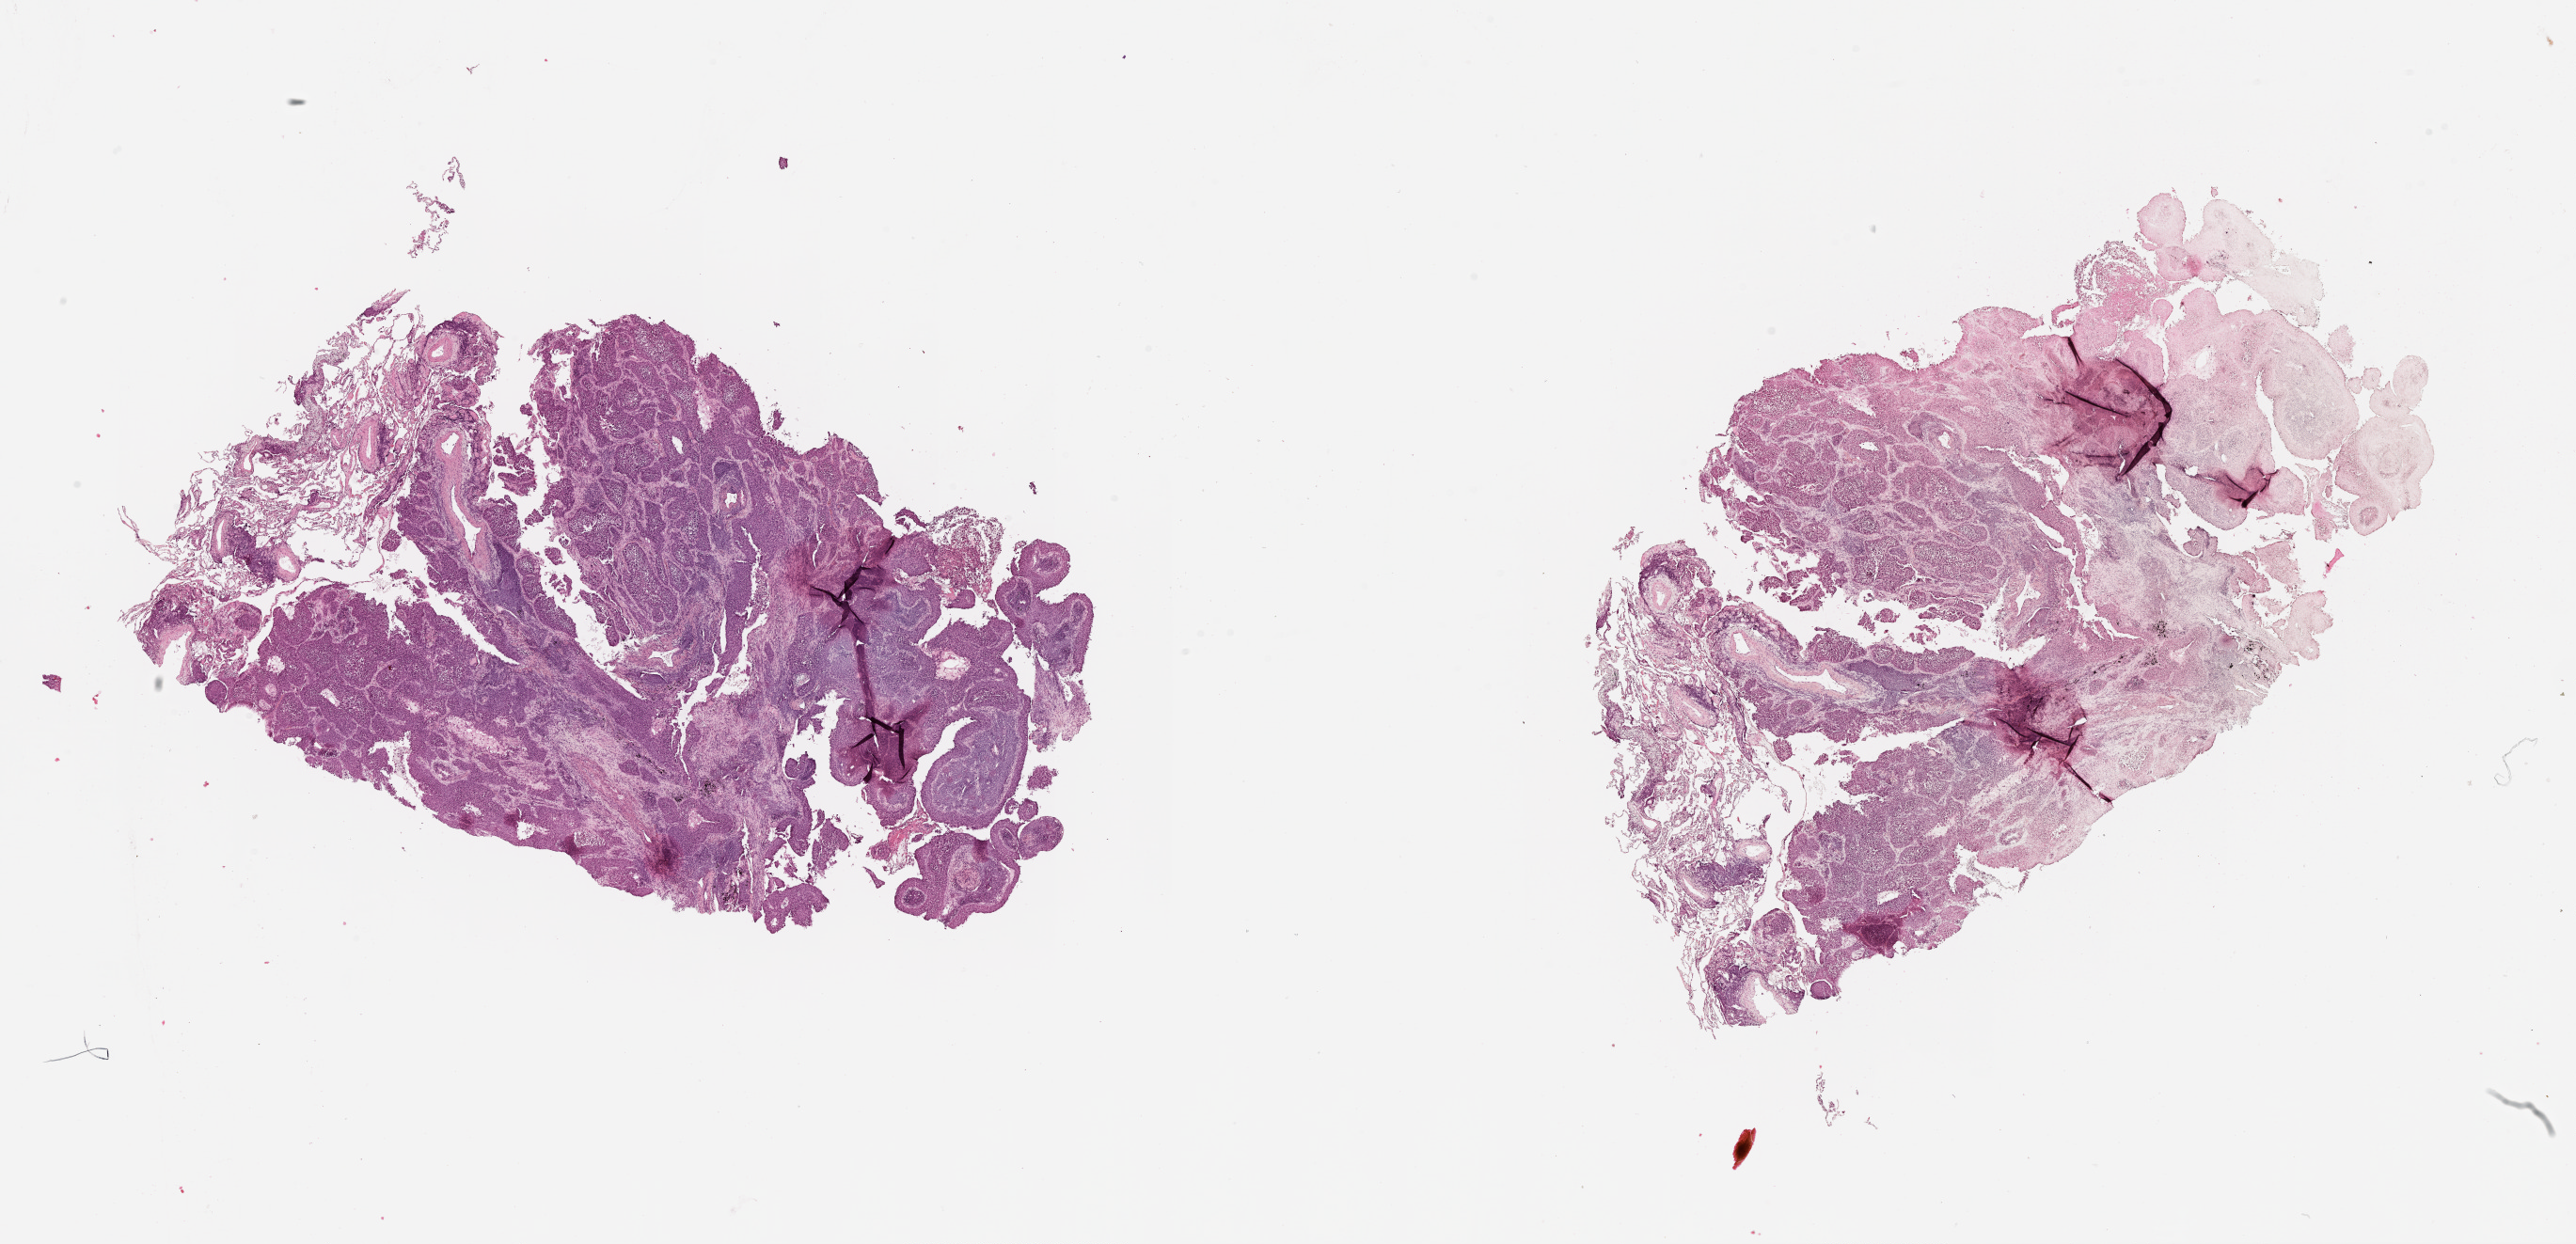
Digitized H&E-stained tissue section (whole slide) — whole scanned area (about 22.0 x 10.6 mm, from a 20x scan) shown as a low-resolution overview, tumour tissue sample, lung. Patient: female, age 74 years.
Patient diagnosis (cohort enrolment): squamous cell carcinoma (lung).